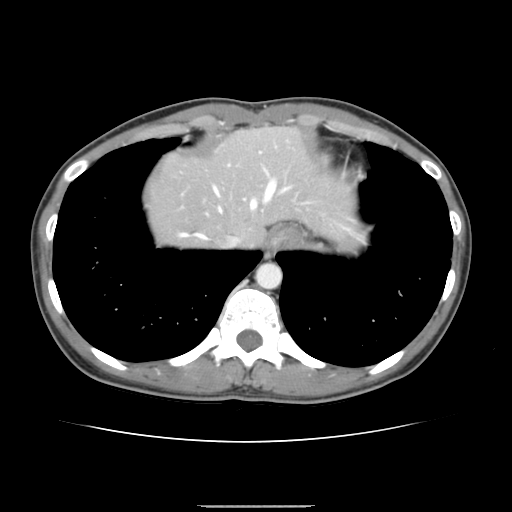
Contrast-enhanced abdominal CT, one axial slice. Position 126 of 150 along the scan axis. Intravenous contrast given. Soft-tissue window (W 400 / L 40 HU). 2.5 mm slice thickness. 512 × 512 image matrix, field of view 324 × 324 mm. Female patient, age 32 years. Case-level facts recorded for this patient, not image findings: diagnosis: colorectal cancer liver metastases, imaged before liver resection; multiple liver metastases: yes; largest metastasis: 0.7 cm; disease in both lobes: no.
Outlined on this slice (manually delineated by an expert):
- hepatic veins: bounding box [x1, y1, x2, y2] px = [180, 179, 288, 246]
- liver: [147, 127, 346, 247]
- planned liver remnant (the part of the liver to remain after resection): [147, 128, 346, 245]
- portal vein (with intrahepatic branches): [228, 152, 261, 165]